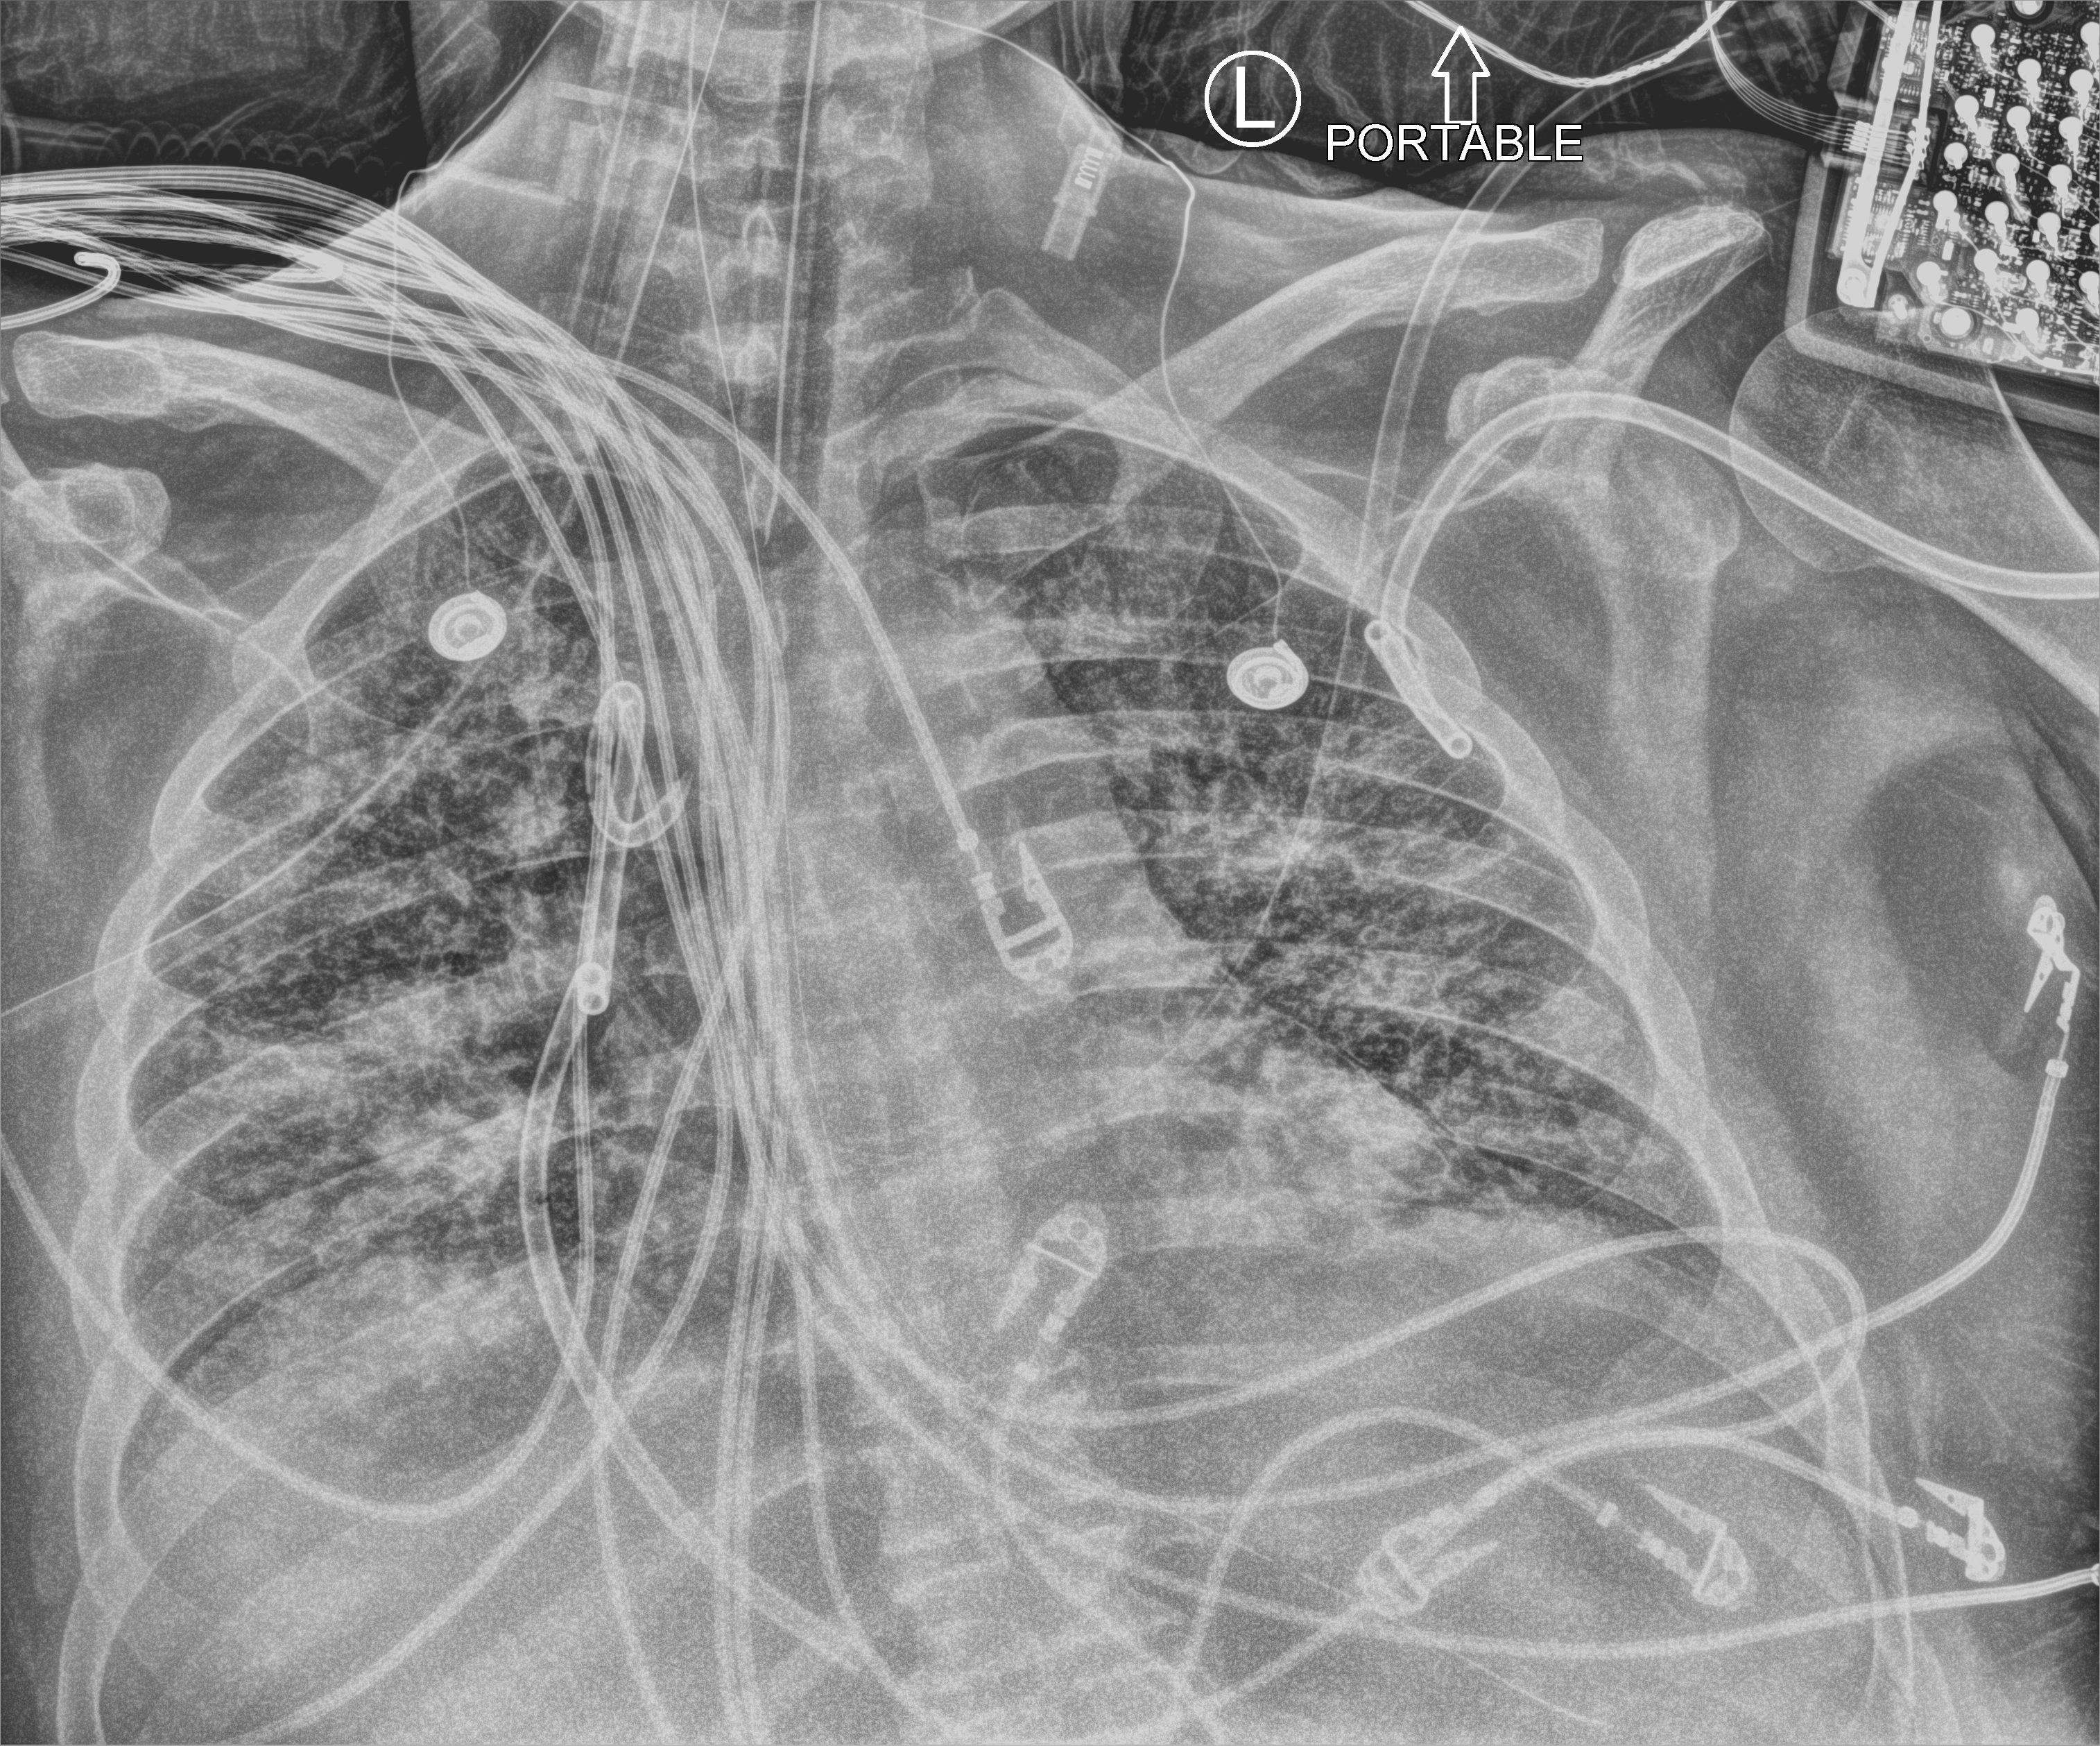
Portable chest radiograph, anteroposterior (AP) projection. Adult patient hospitalised with COVID-19, age 18–59 years.
From the hospital-stay record, not from the radiograph (when in the stay this image was taken is not recorded): admitted to intensive care during this hospital stay: yes; mechanically ventilated during this hospital stay: yes.